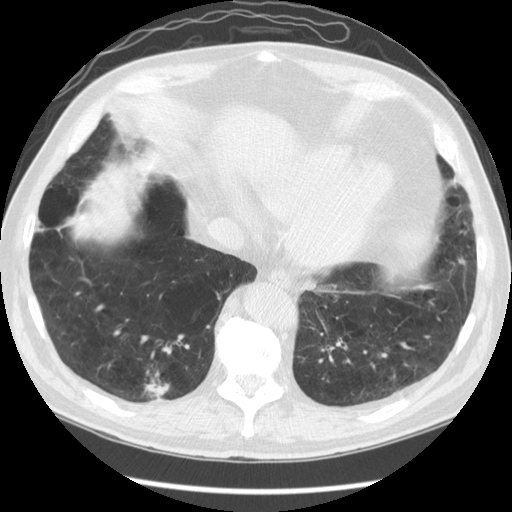
Chest CT (low-dose screening protocol), one axial image. Baseline screening round. Lung window (W 1500 / L -600 HU). 2.5 mm slice thickness. 120 kVp. Slice 101 of 141 in the series. Male, age 67 years at enrolment.
Lesion marked by an expert reader, box from (x=121, y=356) to (x=184, y=413) px. The screening reader recorded 2 non-calcified nodules or masses ≥4 mm on this exam; which of them this box marks is not recorded. Official screen result: positive, change unspecified: nodule(s) >= 4 mm or enlarging nodule(s), mass(es), or other non-specific abnormalities suspicious for lung cancer.